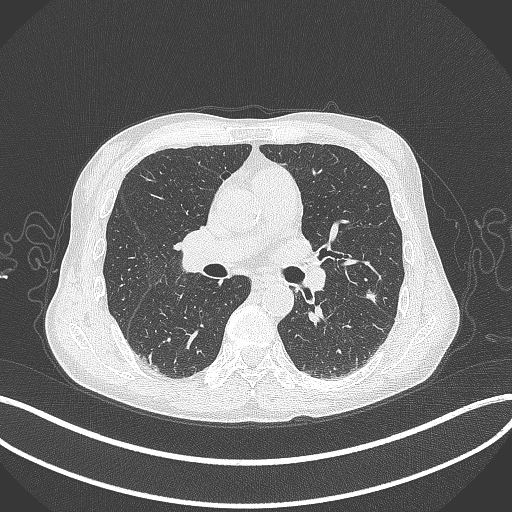
Chest CT, one axial slice. Slice 199 of 429 in the series (ordered by position). Lung window (W 1500 / L -600 HU). 1 mm slice thickness. 512 × 512 image matrix, field of view 400 × 400 mm. Patient: male, 58 years. Case-level facts recorded for this patient, not image findings: clinical TNM (as recorded): T1c N0 M0; histopathological grade: G2.
Structures marked on this image (bounding box drawn by a radiologist):
- lung tumour (recorded histology: adenocarcinoma): box from (x=362, y=286) to (x=380, y=303) px